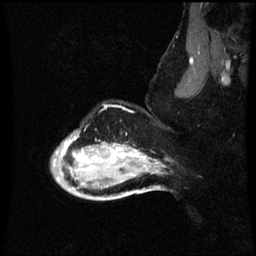
Breast MRI (dynamic contrast-enhanced), one sagittal slice; slice 49 of 60 in the series (ordered by position); dynamic contrast-enhanced series, image 2 of 3 at this slice position (ordered by acquisition); 1.5 T; TE 4.2 ms, TR 8.9 ms; 2 mm slice thickness; 256 × 256 image matrix, field of view 200 × 200 mm. Female patient, age 49 years. From the clinical record (not read from this slice): setting: breast cancer imaged before/during neoadjuvant chemotherapy; receptor status: HR-positive, HER2-negative.
Outlined on this slice (semi-automatic segmentation, software-assisted and operator-edited):
- analysis volume of interest (the breast-tissue region the enhancement analysis was run in; not a lesion): box from (x=52, y=128) to (x=159, y=199) px
- tumour enhancement mask (voxels above the 70 % enhancement threshold inside the analysis volume of interest): (x=62, y=138)–(x=147, y=173)